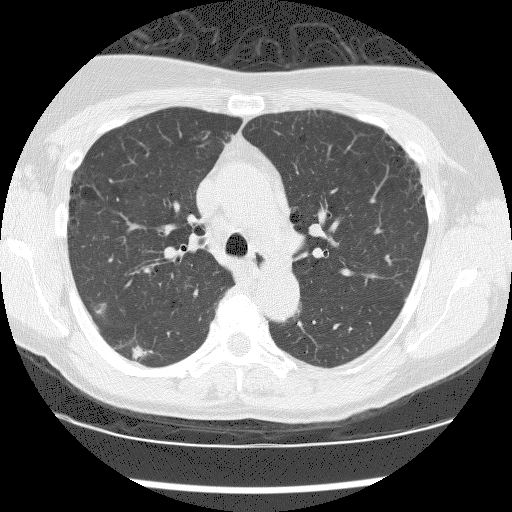
Low-dose screening chest CT, one axial slice. Reconstruction kernel BONE. 120 kVp. Lung window (W 1500 / L -600 HU). 512 × 512 image matrix, field of view 320 × 320 mm.
Annotated regions visible in this slice (expert manual segmentation):
- lesion 1 (tumor, lower lobe of right lung): box from (x=132, y=346) to (x=152, y=360) px